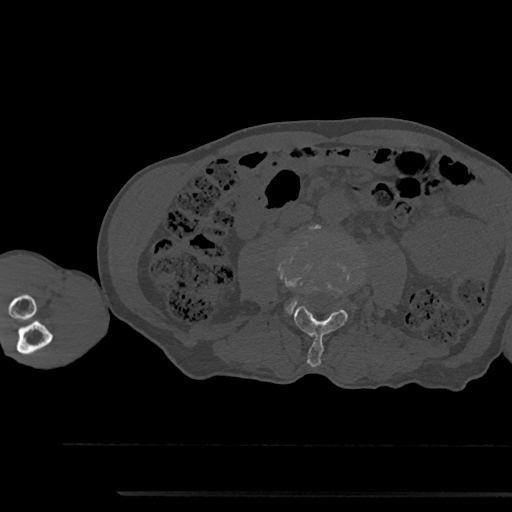
CT including the spine, one axial slice. Slice 459 of 797 in the series (ordered by position). 120 kVp. Bone window (W 1800 / L 400 HU). 0.5 mm slice thickness. 512 × 512 image matrix, field of view 367 × 367 mm. Male patient, age 79 years. Case-level facts recorded for this patient, not image findings: primary cancer: prostate.
Structures marked on this image (semi-automatically segmented with operator editing):
- L3 vertebra: box from (x=294, y=275) to (x=362, y=367) px
- L4 vertebra: (x=288, y=300)–(x=297, y=313)